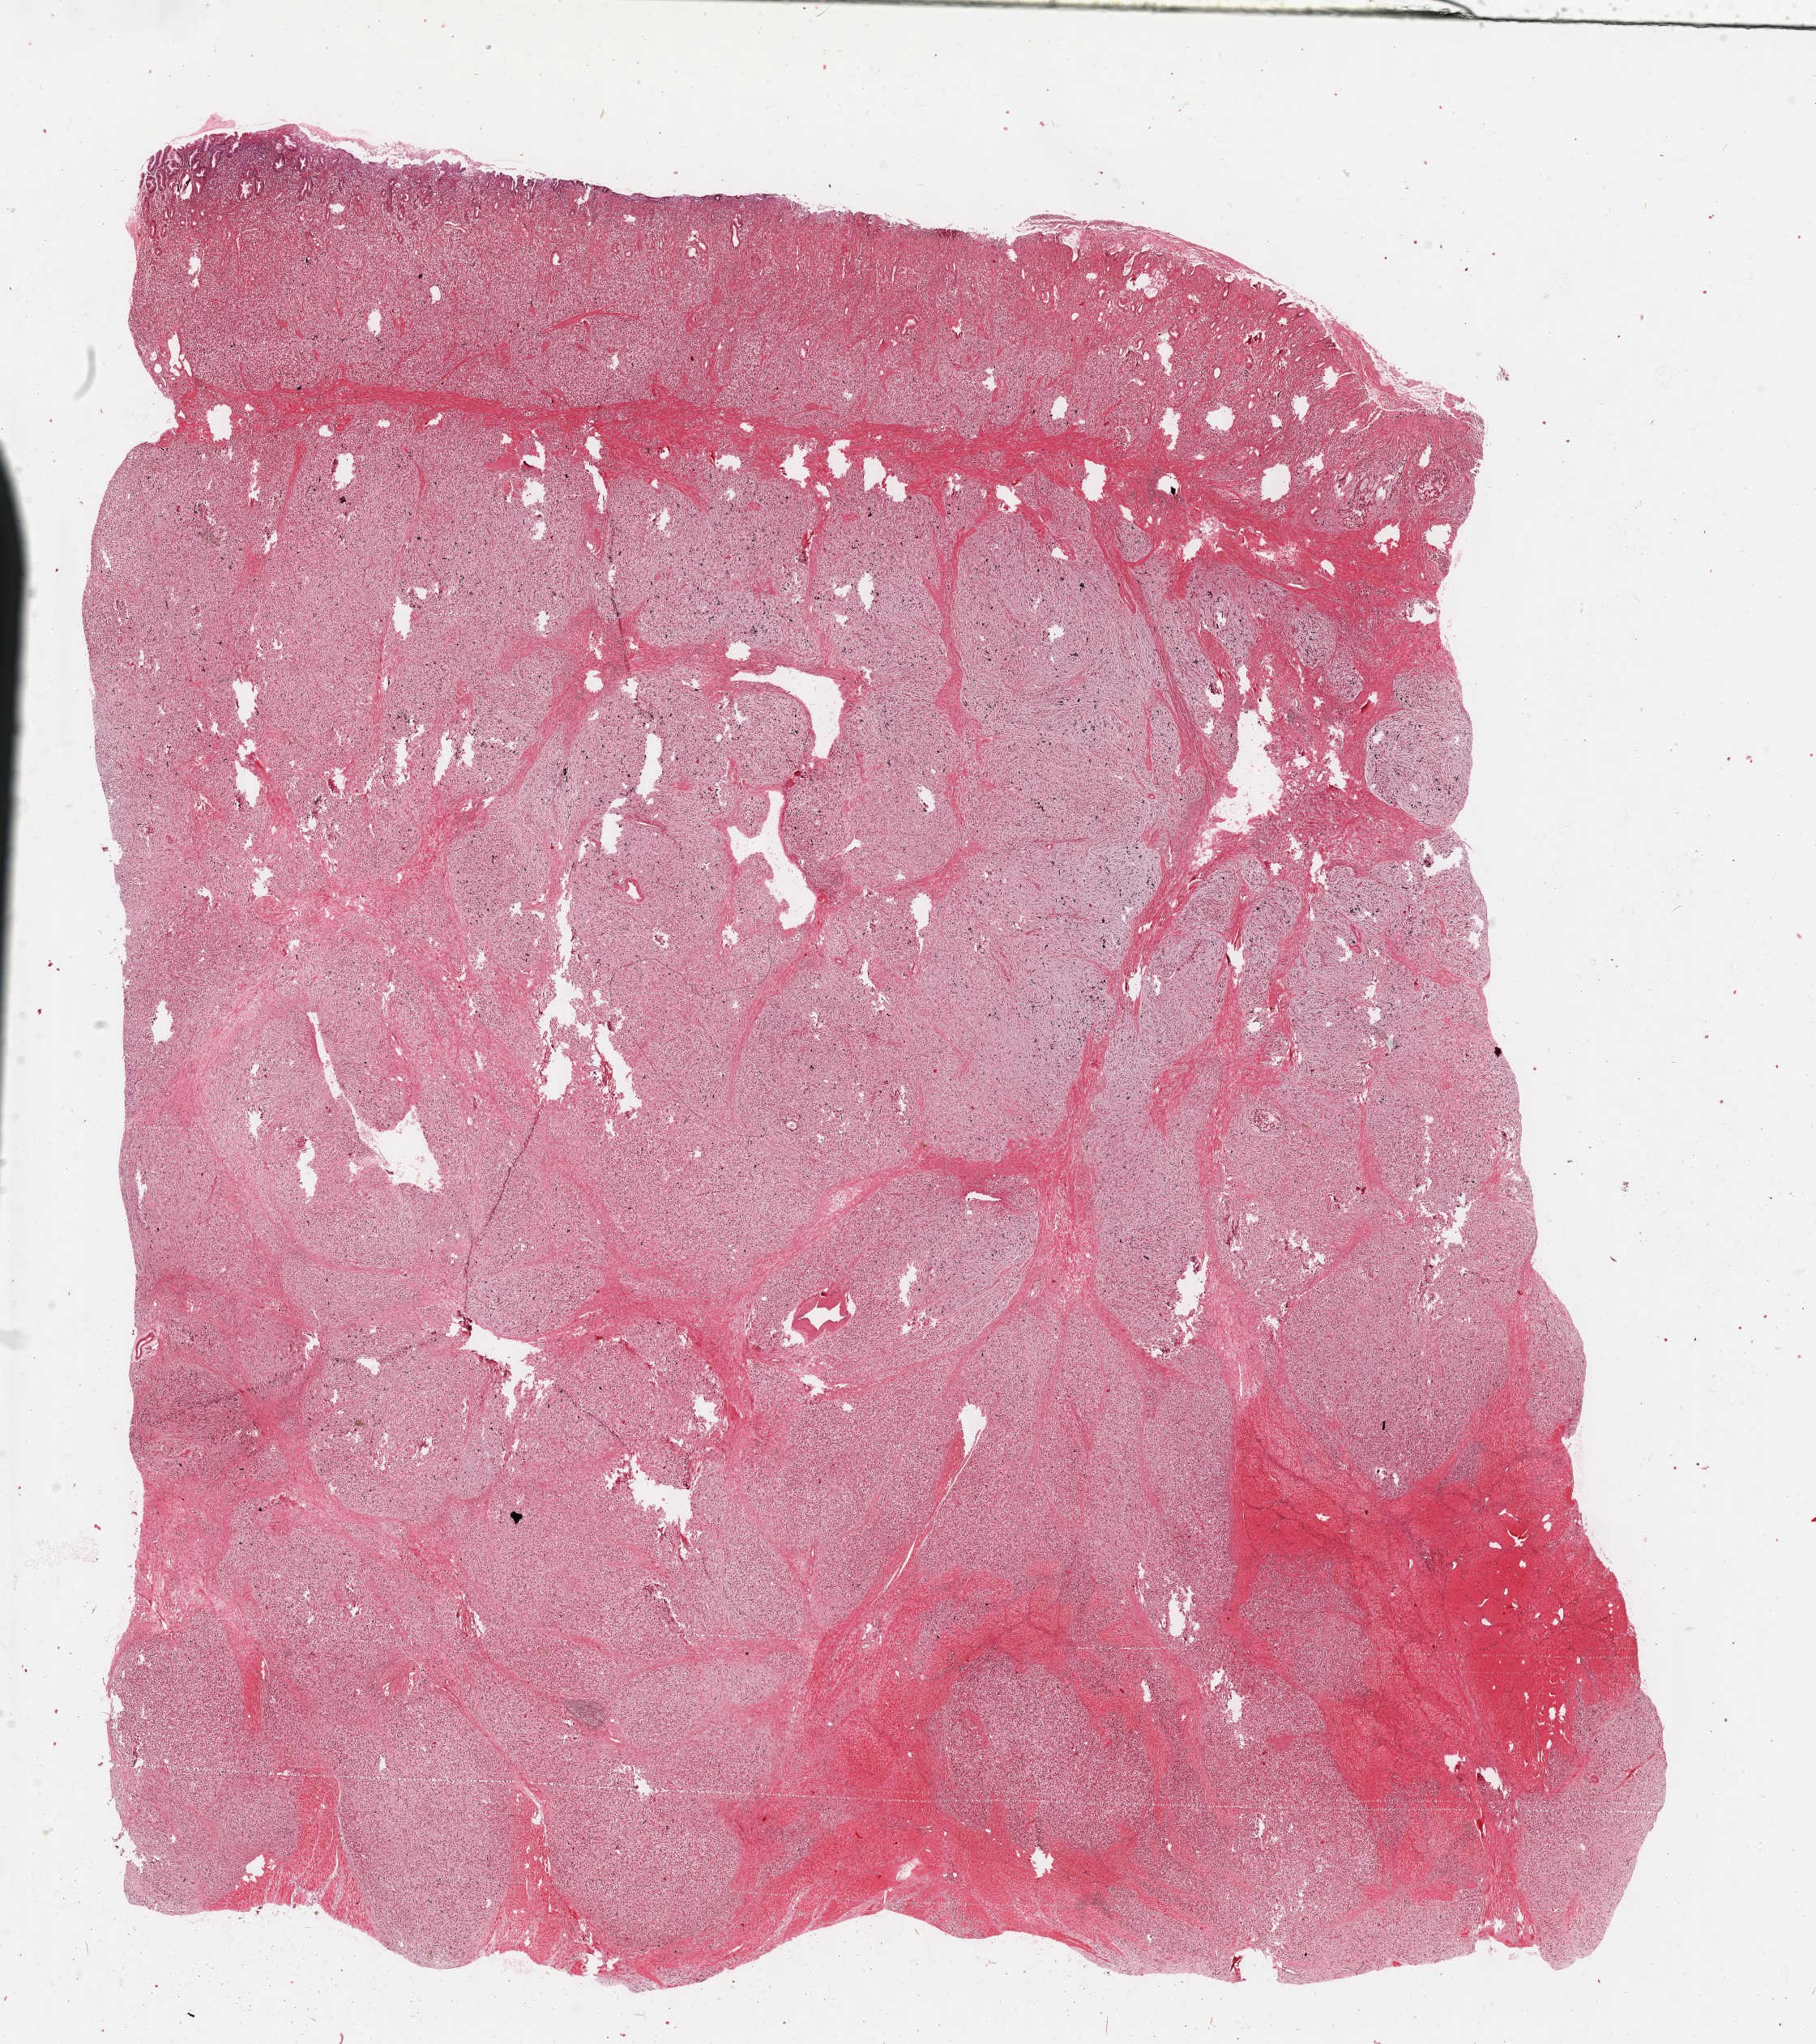
H&E-stained whole-slide image, low-resolution overview of the scanned area, about 18.1 x 20.4 mm. Formalin-fixed paraffin-embedded (FFPE) diagnostic section. Sample: primary tumour, stomach. Male, age 51 years at initial diagnosis. Histologic grade: G3 (poorly differentiated).
Histologic diagnosis: Carcinoma, diffuse type (fundus of stomach). AJCC pathologic stage: II (6th edition).